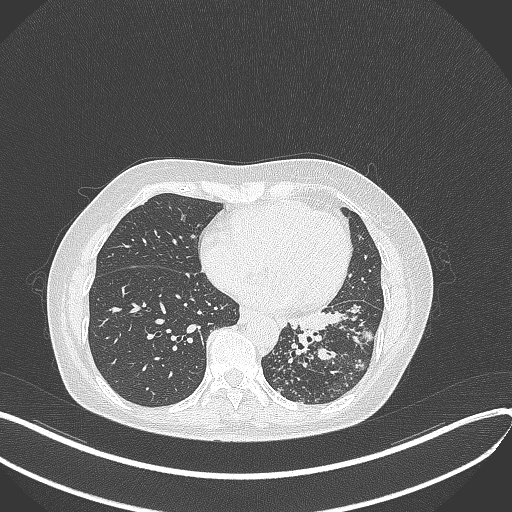
Chest CT, one axial slice; slice 149 of 429 in the series (ordered by position); 100 kVp; lung window (W 1500 / L -600 HU); 512 × 512 image matrix, field of view 400 × 400 mm. Female patient, age 63 years. Case-level facts recorded for this patient, not image findings: clinical TNM (as recorded): T1b N0 M0.
Outlined on this slice (rectangle marked by the reading radiologist):
- lung tumour (recorded histology: adenocarcinoma): box from (x=285, y=309) to (x=373, y=342) px